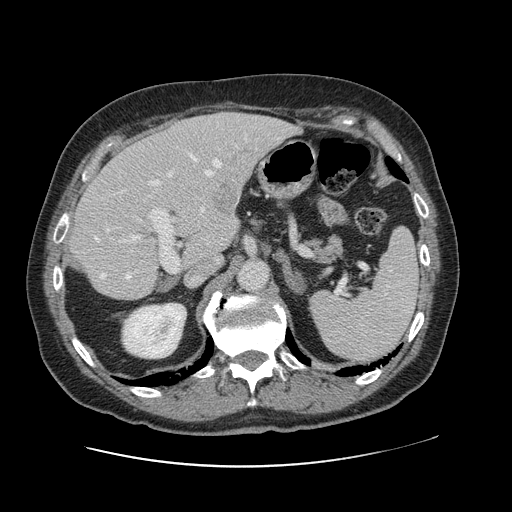
Contrast-enhanced abdominal CT, one axial slice. Position 72 of 138 along the scan axis. 120 kVp. Intravenous contrast given. Soft-tissue window (W 400 / L 40 HU). 2.5 mm slice thickness. 512 × 512 image matrix, field of view 402 × 402 mm. Male patient, age 71 years. From the clinical record (not read from this slice): diagnosis: colorectal cancer liver metastases, imaged before liver resection; multiple liver metastases: no; largest metastasis: 3.3 cm; disease in both lobes: no.
Structures marked on this image (manually delineated by an expert):
- hepatic veins: box from (x=95, y=154) to (x=223, y=279) px
- liver: (x=71, y=114)–(x=294, y=300)
- planned liver remnant (the part of the liver to remain after resection): (x=71, y=147)–(x=227, y=300)
- portal vein (with intrahepatic branches): (x=118, y=170)–(x=179, y=273)
- liver metastasis: (x=212, y=184)–(x=238, y=216)